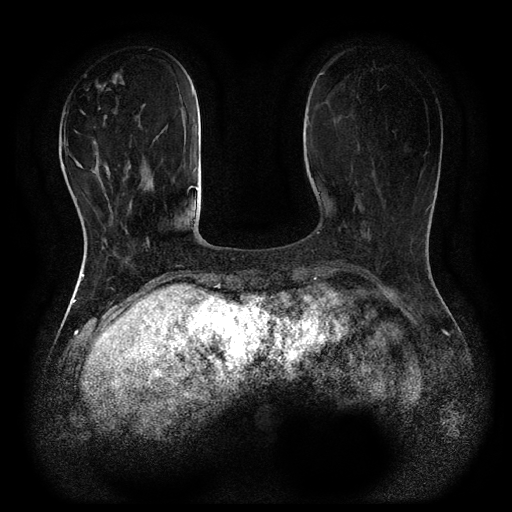
Breast MRI (dynamic contrast-enhanced, multi-phase), one axial slice; position 26 of 116 along the scan axis; dynamic contrast-enhanced series, time point 2 of 5 at this slice position (early post-contrast); 1.5 T; TE 2.6 ms, TR 5.4 ms; 512 × 512 image matrix. Female patient, age 48 years.
Structures marked on this image (semi-automatically segmented with operator editing):
- breast lesion (labelled benign in the annotation): bounding box [x1, y1, x2, y2] px = [95, 69, 125, 91]